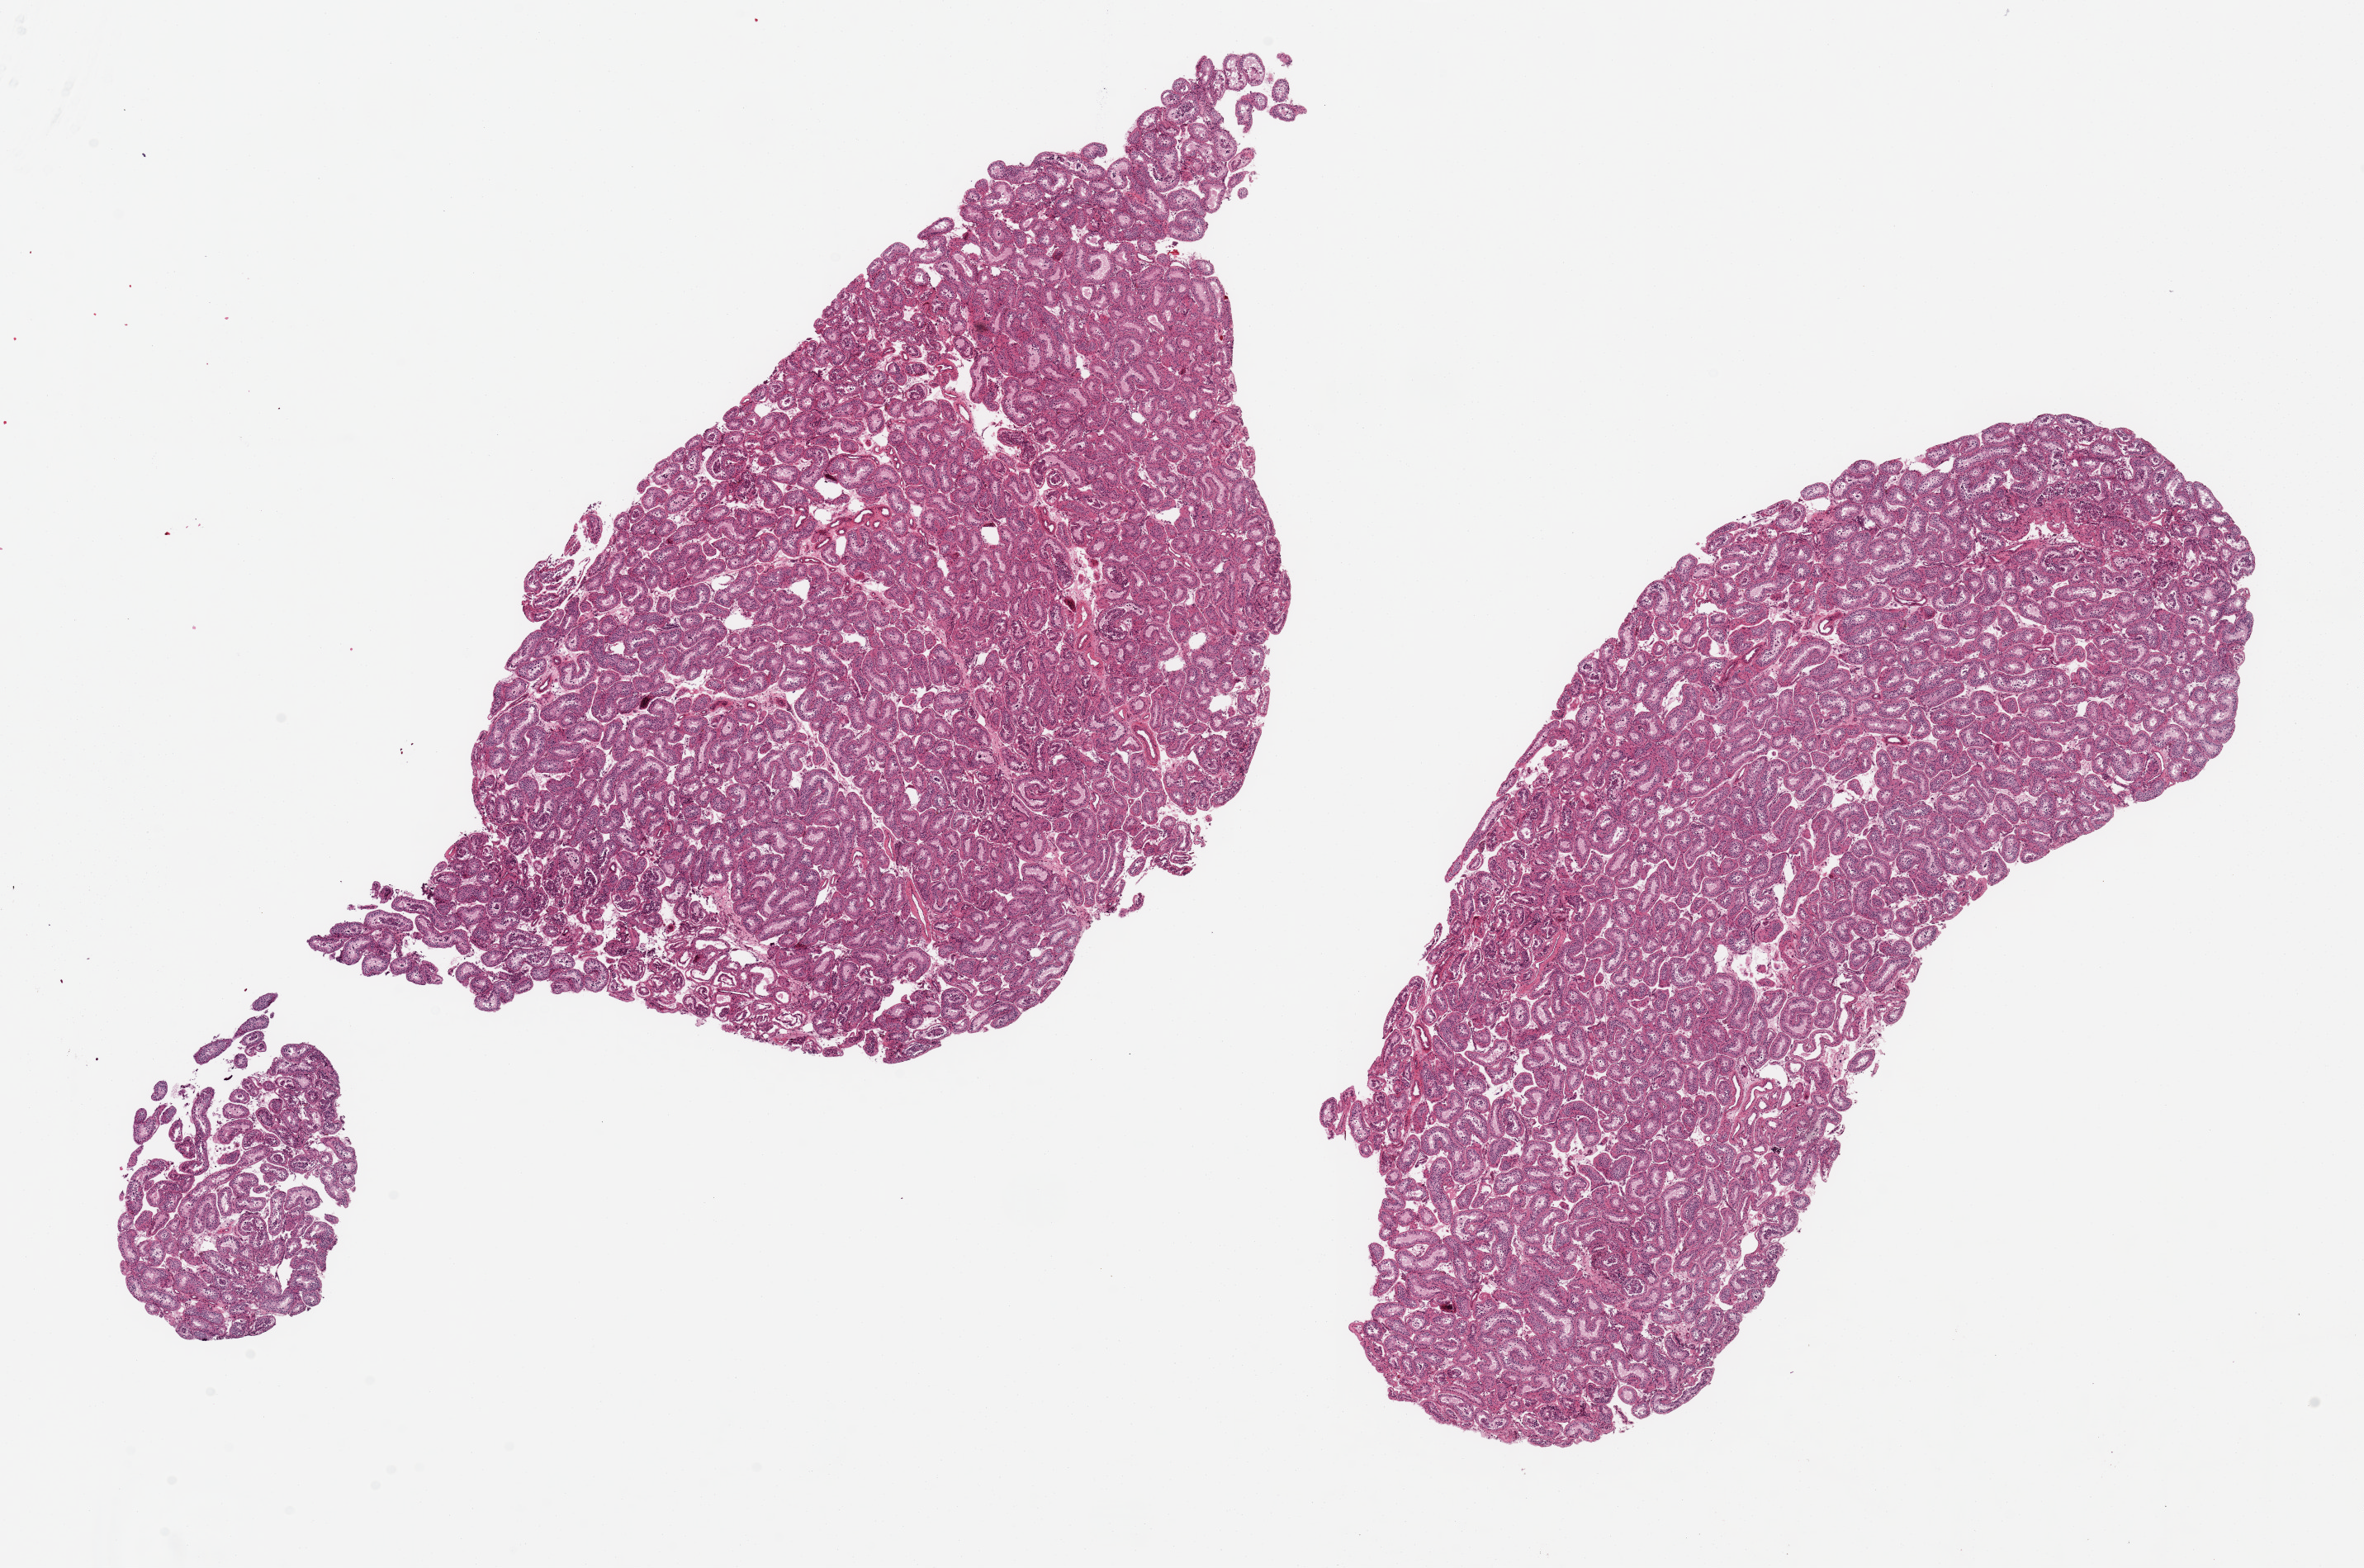
Digitized hematoxylin and eosin (H&E)-stained section — low-resolution overview of the scanned area, about 22.6 x 15.0 mm (from a 20x scan). PAXgene-fixed, paraffin-embedded tissue. Sampled site (target tissue): testis. Tissue donor sample. Donor sex: male.
* pathologist's review note for this sample: 2 ~11x5mm aliquots. Spermatogenesis appears reduced/arrested